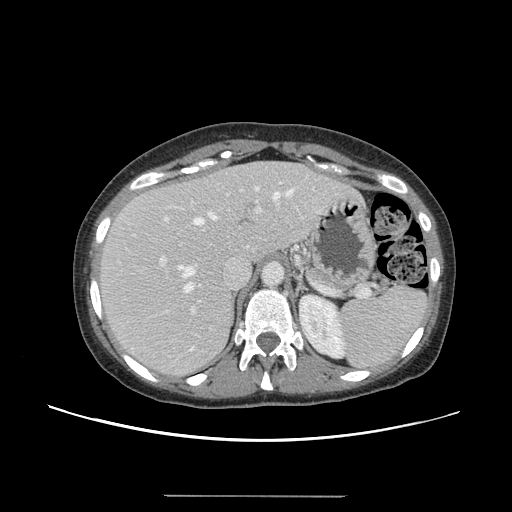
Contrast-enhanced abdominal CT, one axial slice; slice 102 of 144 in the series (ordered by position); 120 kVp; intravenous contrast given; soft-tissue window (W 400 / L 40 HU); 2.5 mm slice thickness; 512 × 512 image matrix, field of view 380 × 380 mm. Female patient, age 53 years. From the clinical record (not read from this slice): diagnosis: colorectal cancer liver metastases, imaged before liver resection; multiple liver metastases: yes; largest metastasis: 1.1 cm.
Annotated regions visible in this slice (outlined manually by an expert reader):
- hepatic veins: bounding box [x1, y1, x2, y2] px = [178, 187, 291, 291]
- liver: [100, 162, 357, 376]
- planned liver remnant (the part of the liver to remain after resection): [100, 163, 303, 300]
- portal vein (with intrahepatic branches): [160, 182, 282, 314]